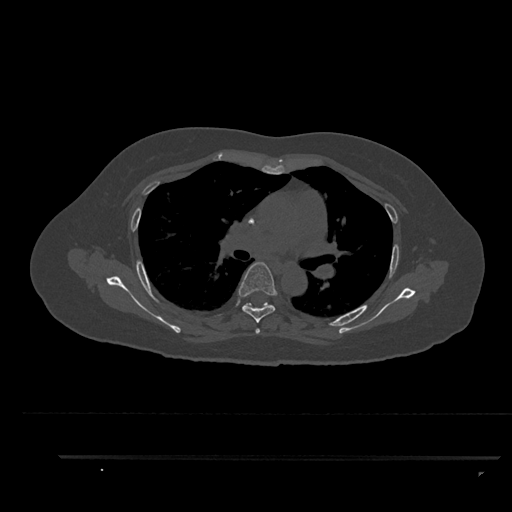
CT including the spine, one axial slice; position 596 of 797 along the scan axis; bone window (W 1800 / L 400 HU); 512 × 512 image matrix, field of view 408 × 408 mm. Patient: female, 44 years. From the clinical record (not read from this slice): primary cancer: renal; vertebrae with lytic lesions (as recorded): L1.
Structures marked on this image (semi-automatically segmented with operator editing):
- T4 vertebra: bounding box [x1, y1, x2, y2] px = [255, 328, 260, 334]
- T5 vertebra: [238, 262, 278, 323]
- T6 vertebra: [242, 302, 270, 308]